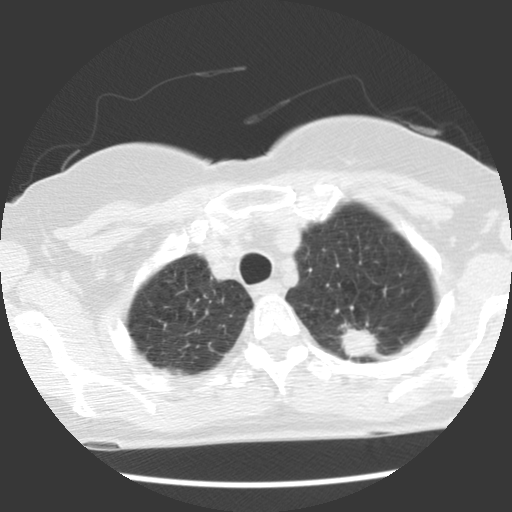
Axial slice from a low-dose chest CT screening exam. Baseline annual screen. Lung window (W 1500 / L -600 HU). 2.5 mm slice thickness. Standard (soft-tissue) reconstruction kernel (STANDARD). 140 kVp. Slice 99 of 120 in the series. 512 × 512 image matrix, field of view 300 × 300 mm. Female participant, aged 66 years at enrolment. Former smoker at enrolment.
Lesion marked by an expert reader, box from (x=319, y=307) to (x=388, y=369) px. Reader record for this screening exam (exam-level; its link to the box is not recorded): non-calcified nodule or mass ≥4 mm, left upper lobe, 22 × 17 mm, spiculated (stellate) margins, soft tissue attenuation. Official screen result: positive, change unspecified: nodule(s) >= 4 mm or enlarging nodule(s), mass(es), or other non-specific abnormalities suspicious for lung cancer.